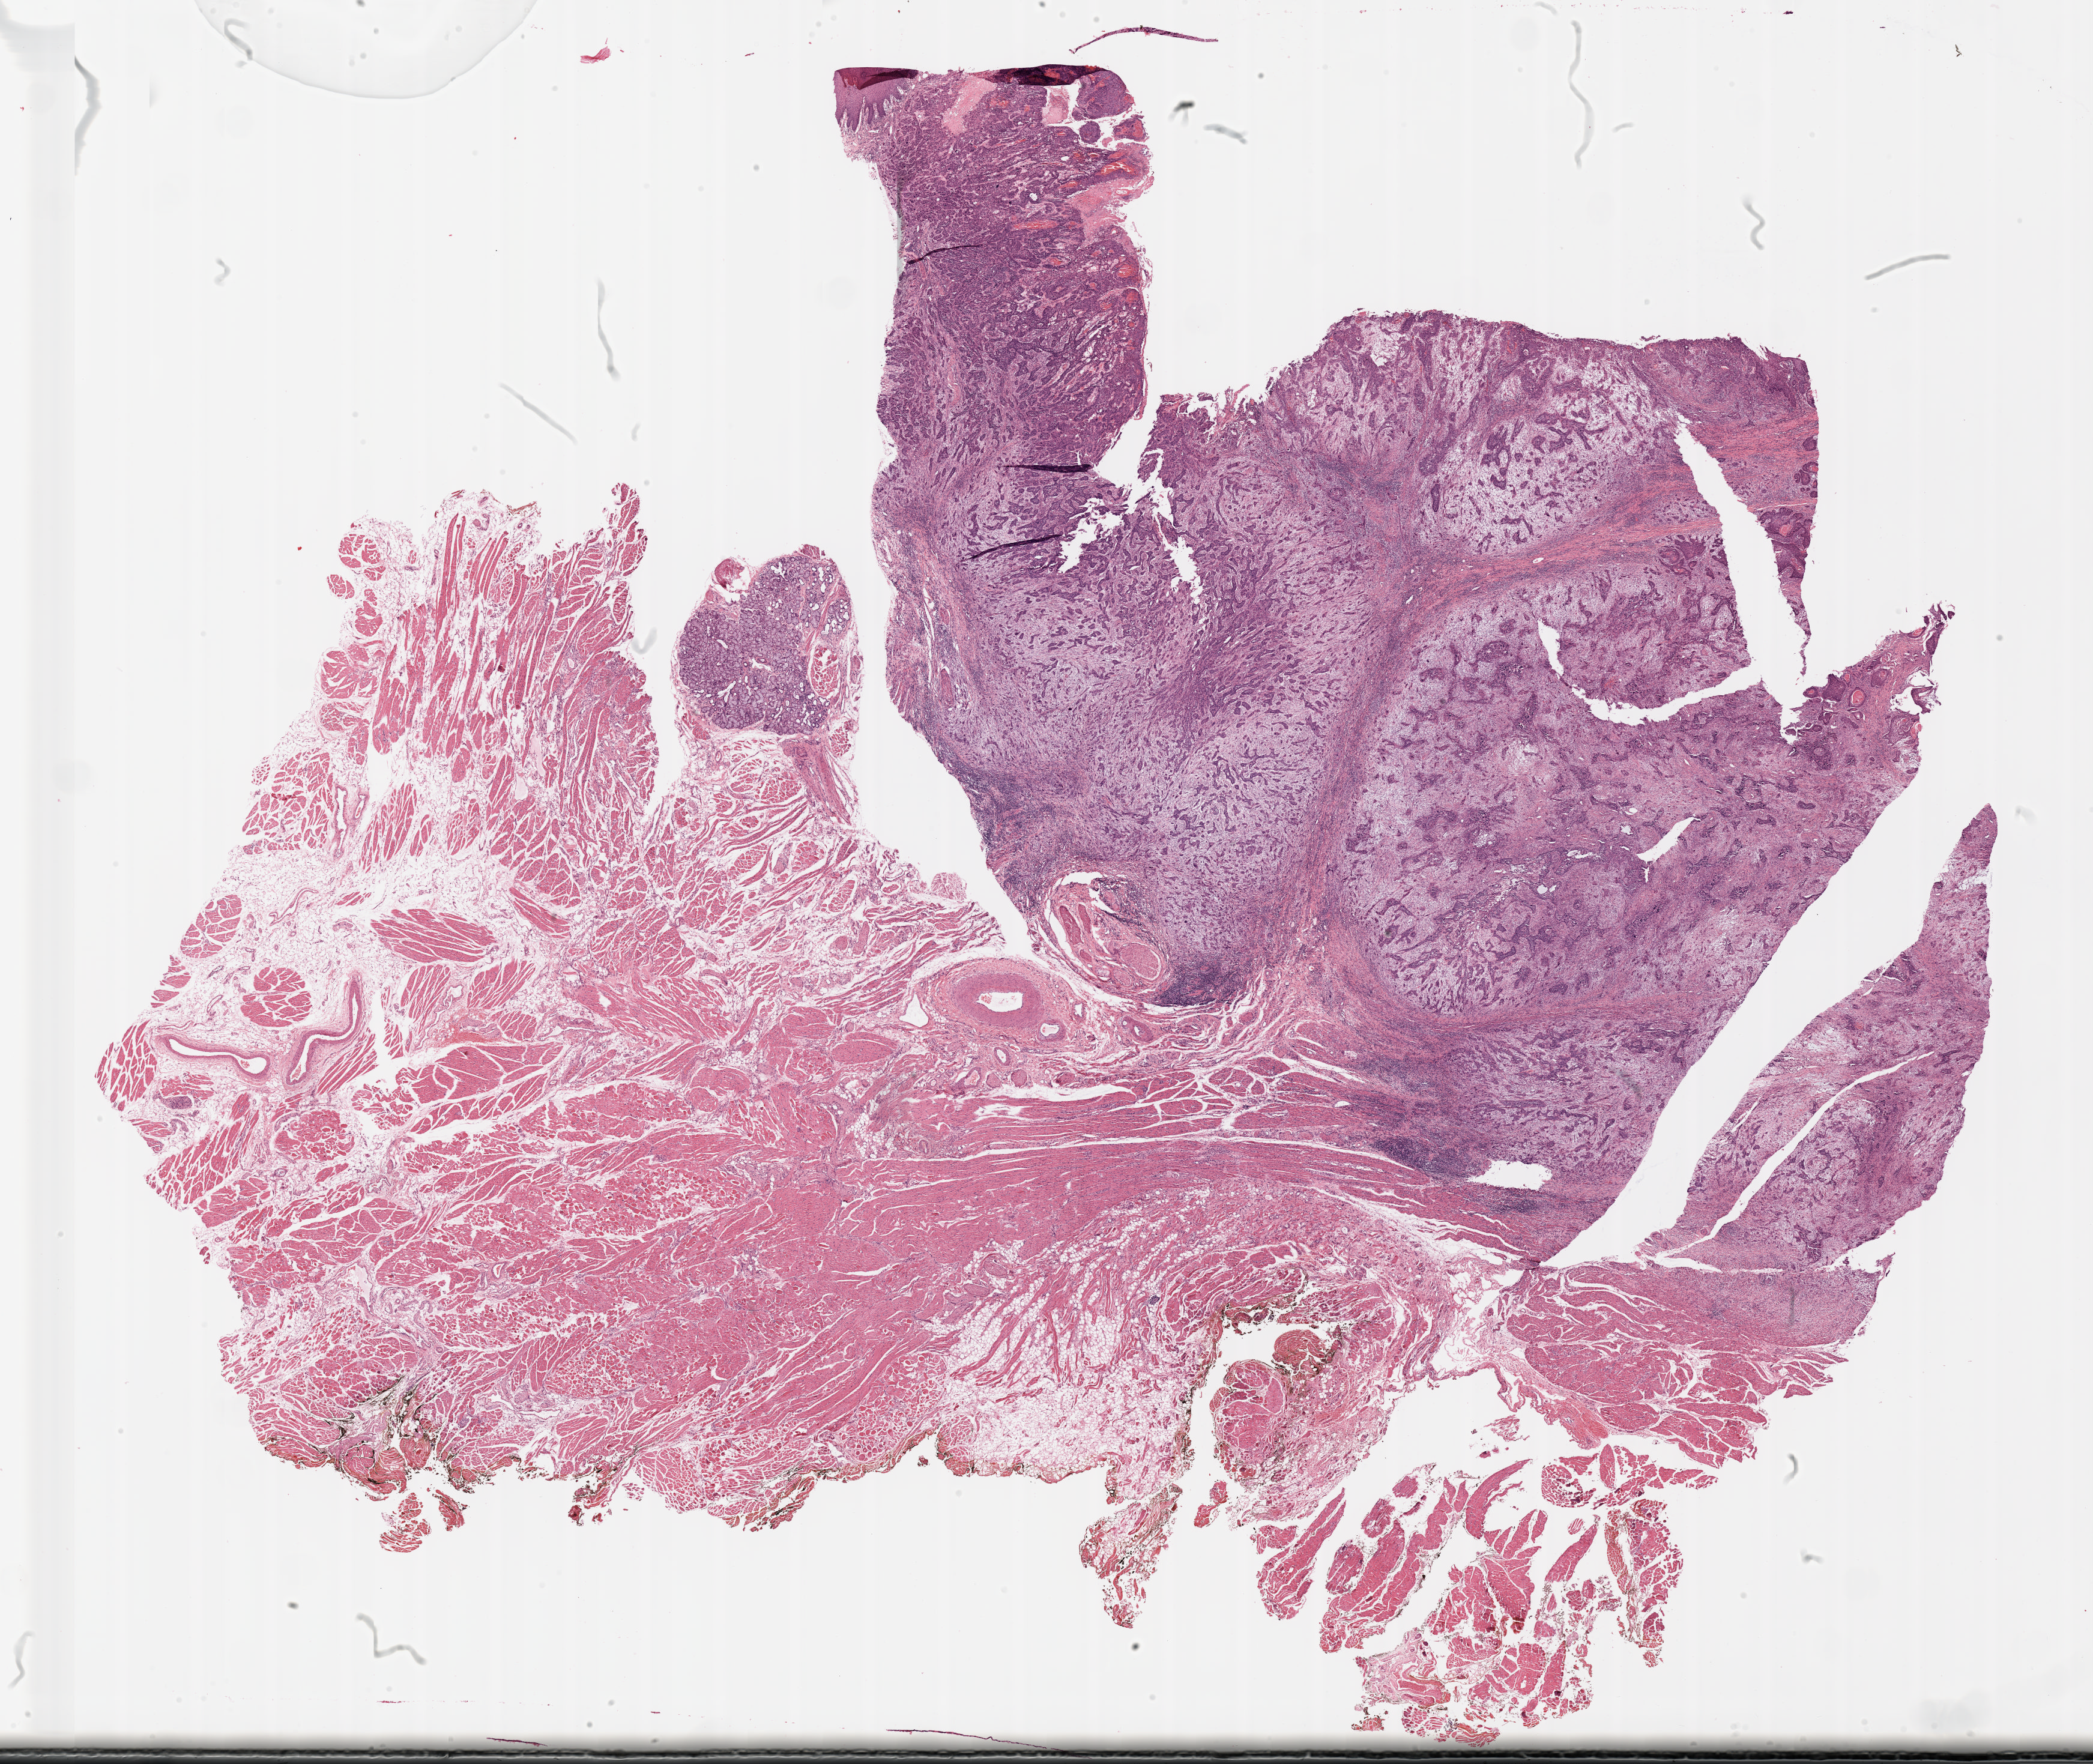
Digitized H&E tissue section (whole slide) — a low-resolution overview of the entire scanned area, about 27.7 x 23.3 mm (slide scanned at 20x), formalin-fixed paraffin-embedded (FFPE) diagnostic section, head and neck, primary tumour sample. Patient: male, age at initial diagnosis 51 years.
Histologic diagnosis: Squamous cell carcinoma, NOS.